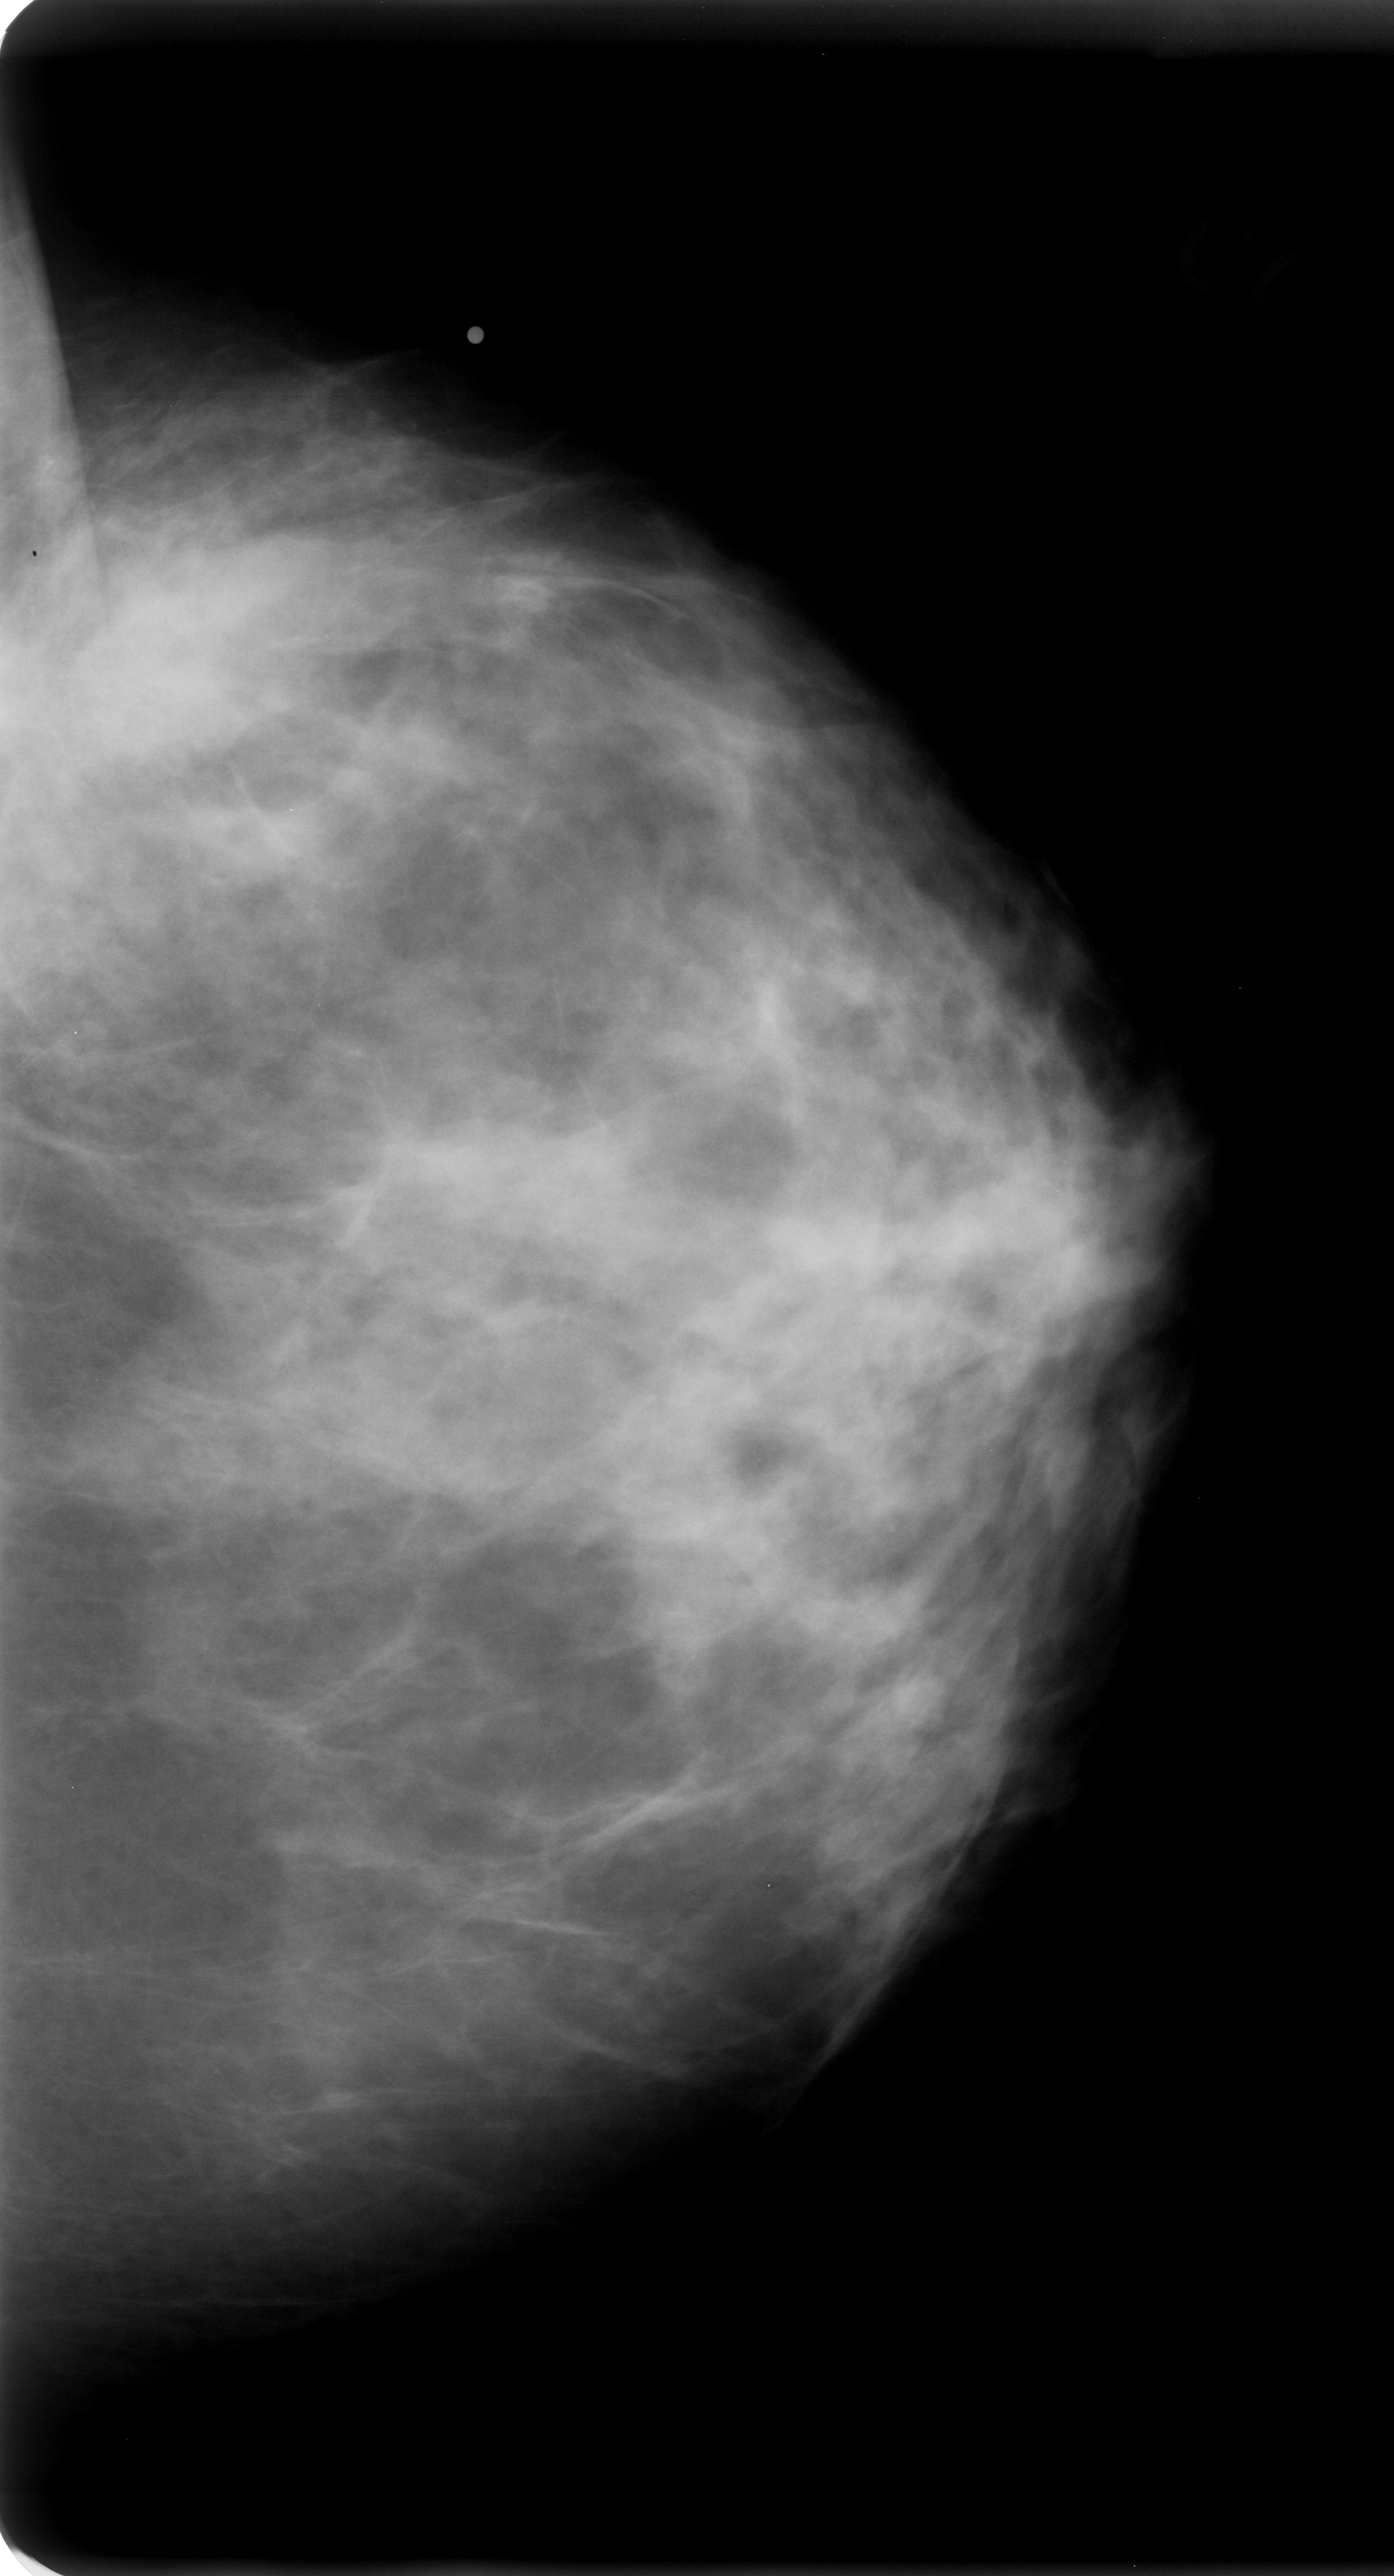
Digitized screen-film mammogram, left breast, CC view, BI-RADS breast density category 3 (scale 1–4).
Marked abnormality: mass, shape irregular, margins ill defined; BI-RADS assessment category 4; subtlety rating 4 on a 1 (subtle) to 5 (obvious) scale; pathology (as recorded): malignant.